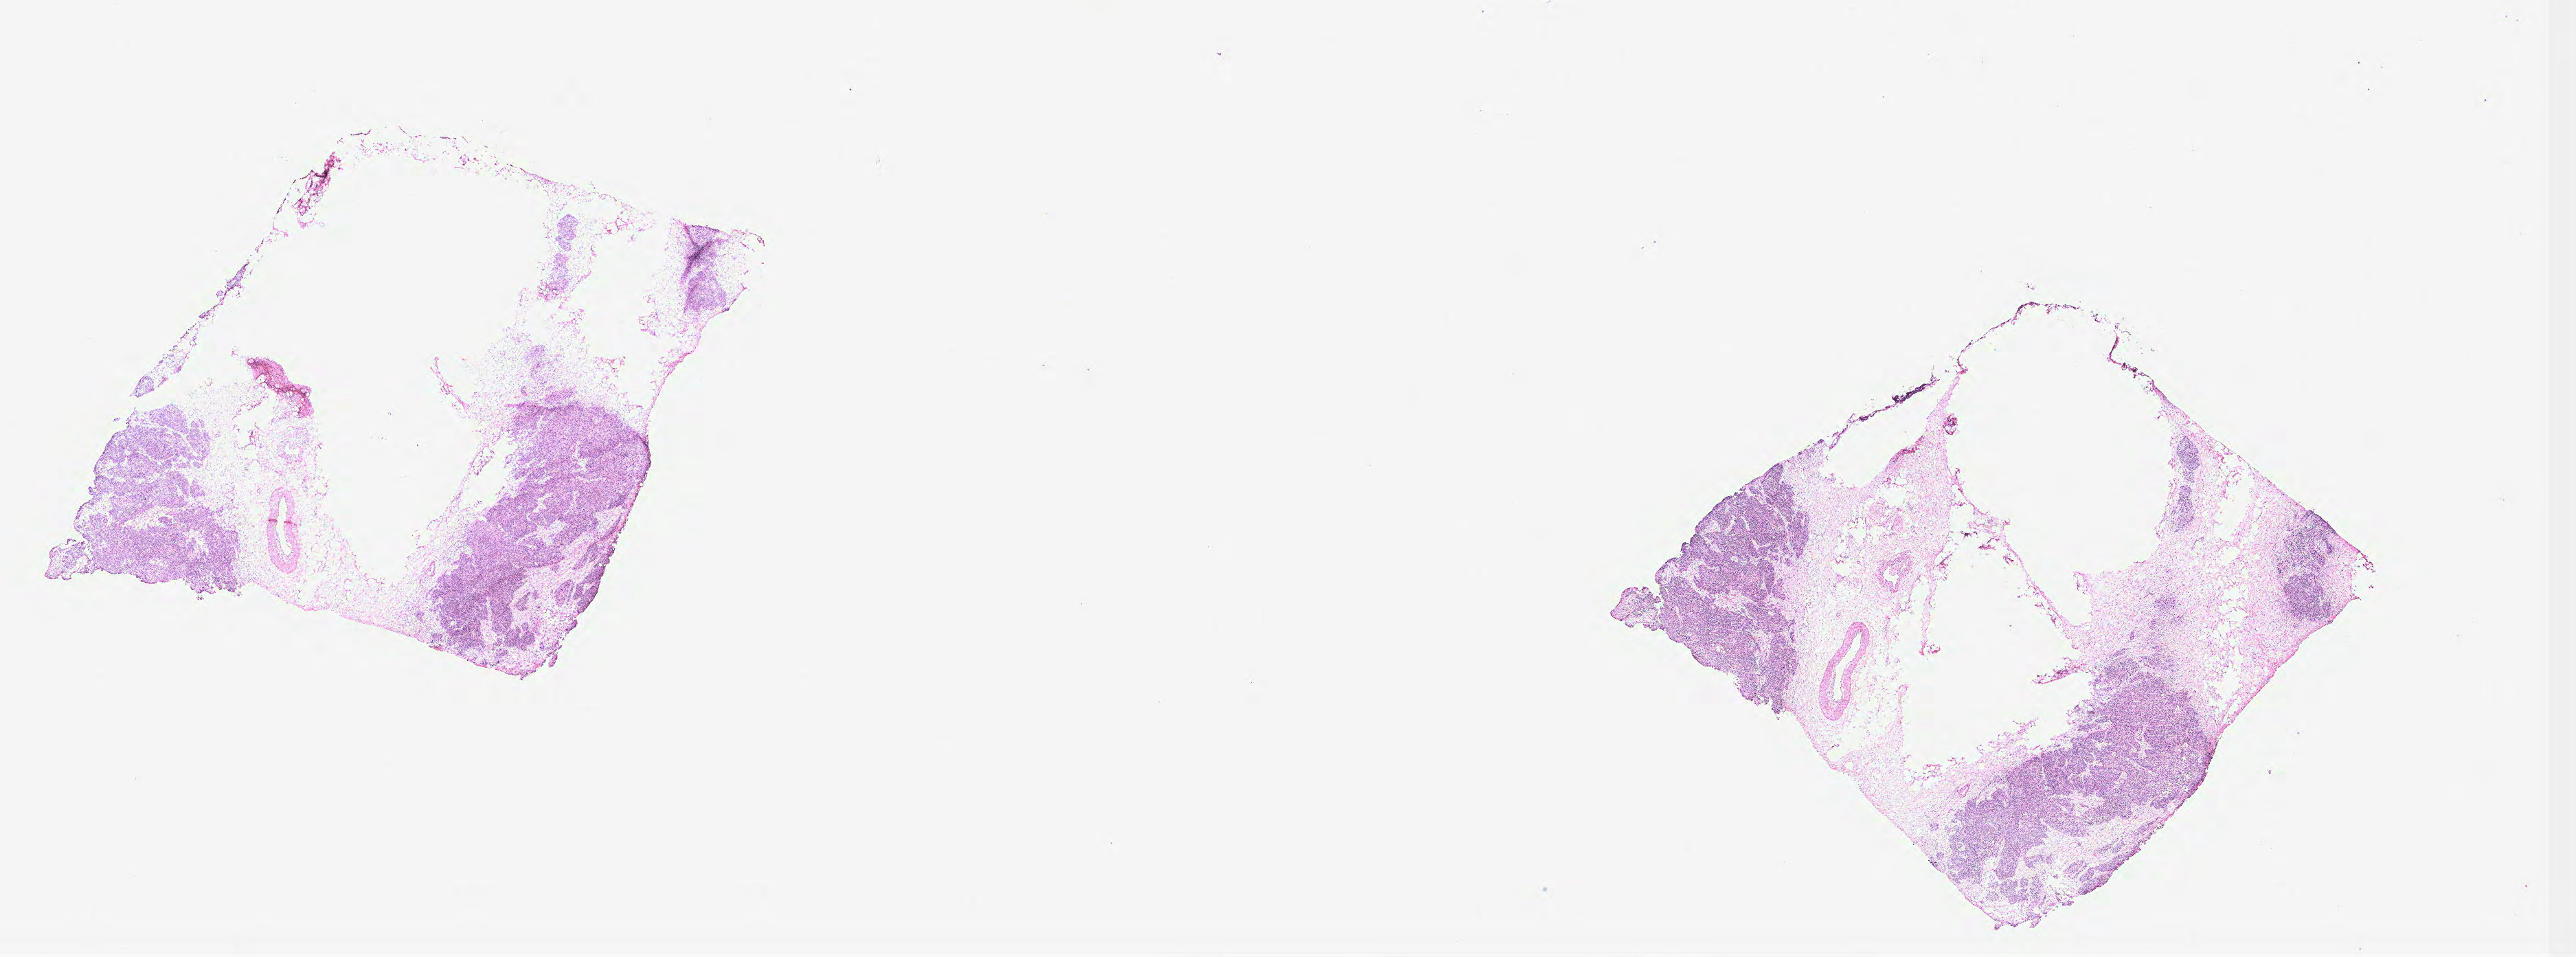
Whole-slide histology image, H&E, shown as a low-resolution overview of the whole scanned area (about 30.0 x 11.1 mm, acquisition: 40x scan); ovary, tissue type not recorded. Patient sex: female.
Patient diagnosis: Serous adenocarcinoma, NOS (peritoneum, NOS).